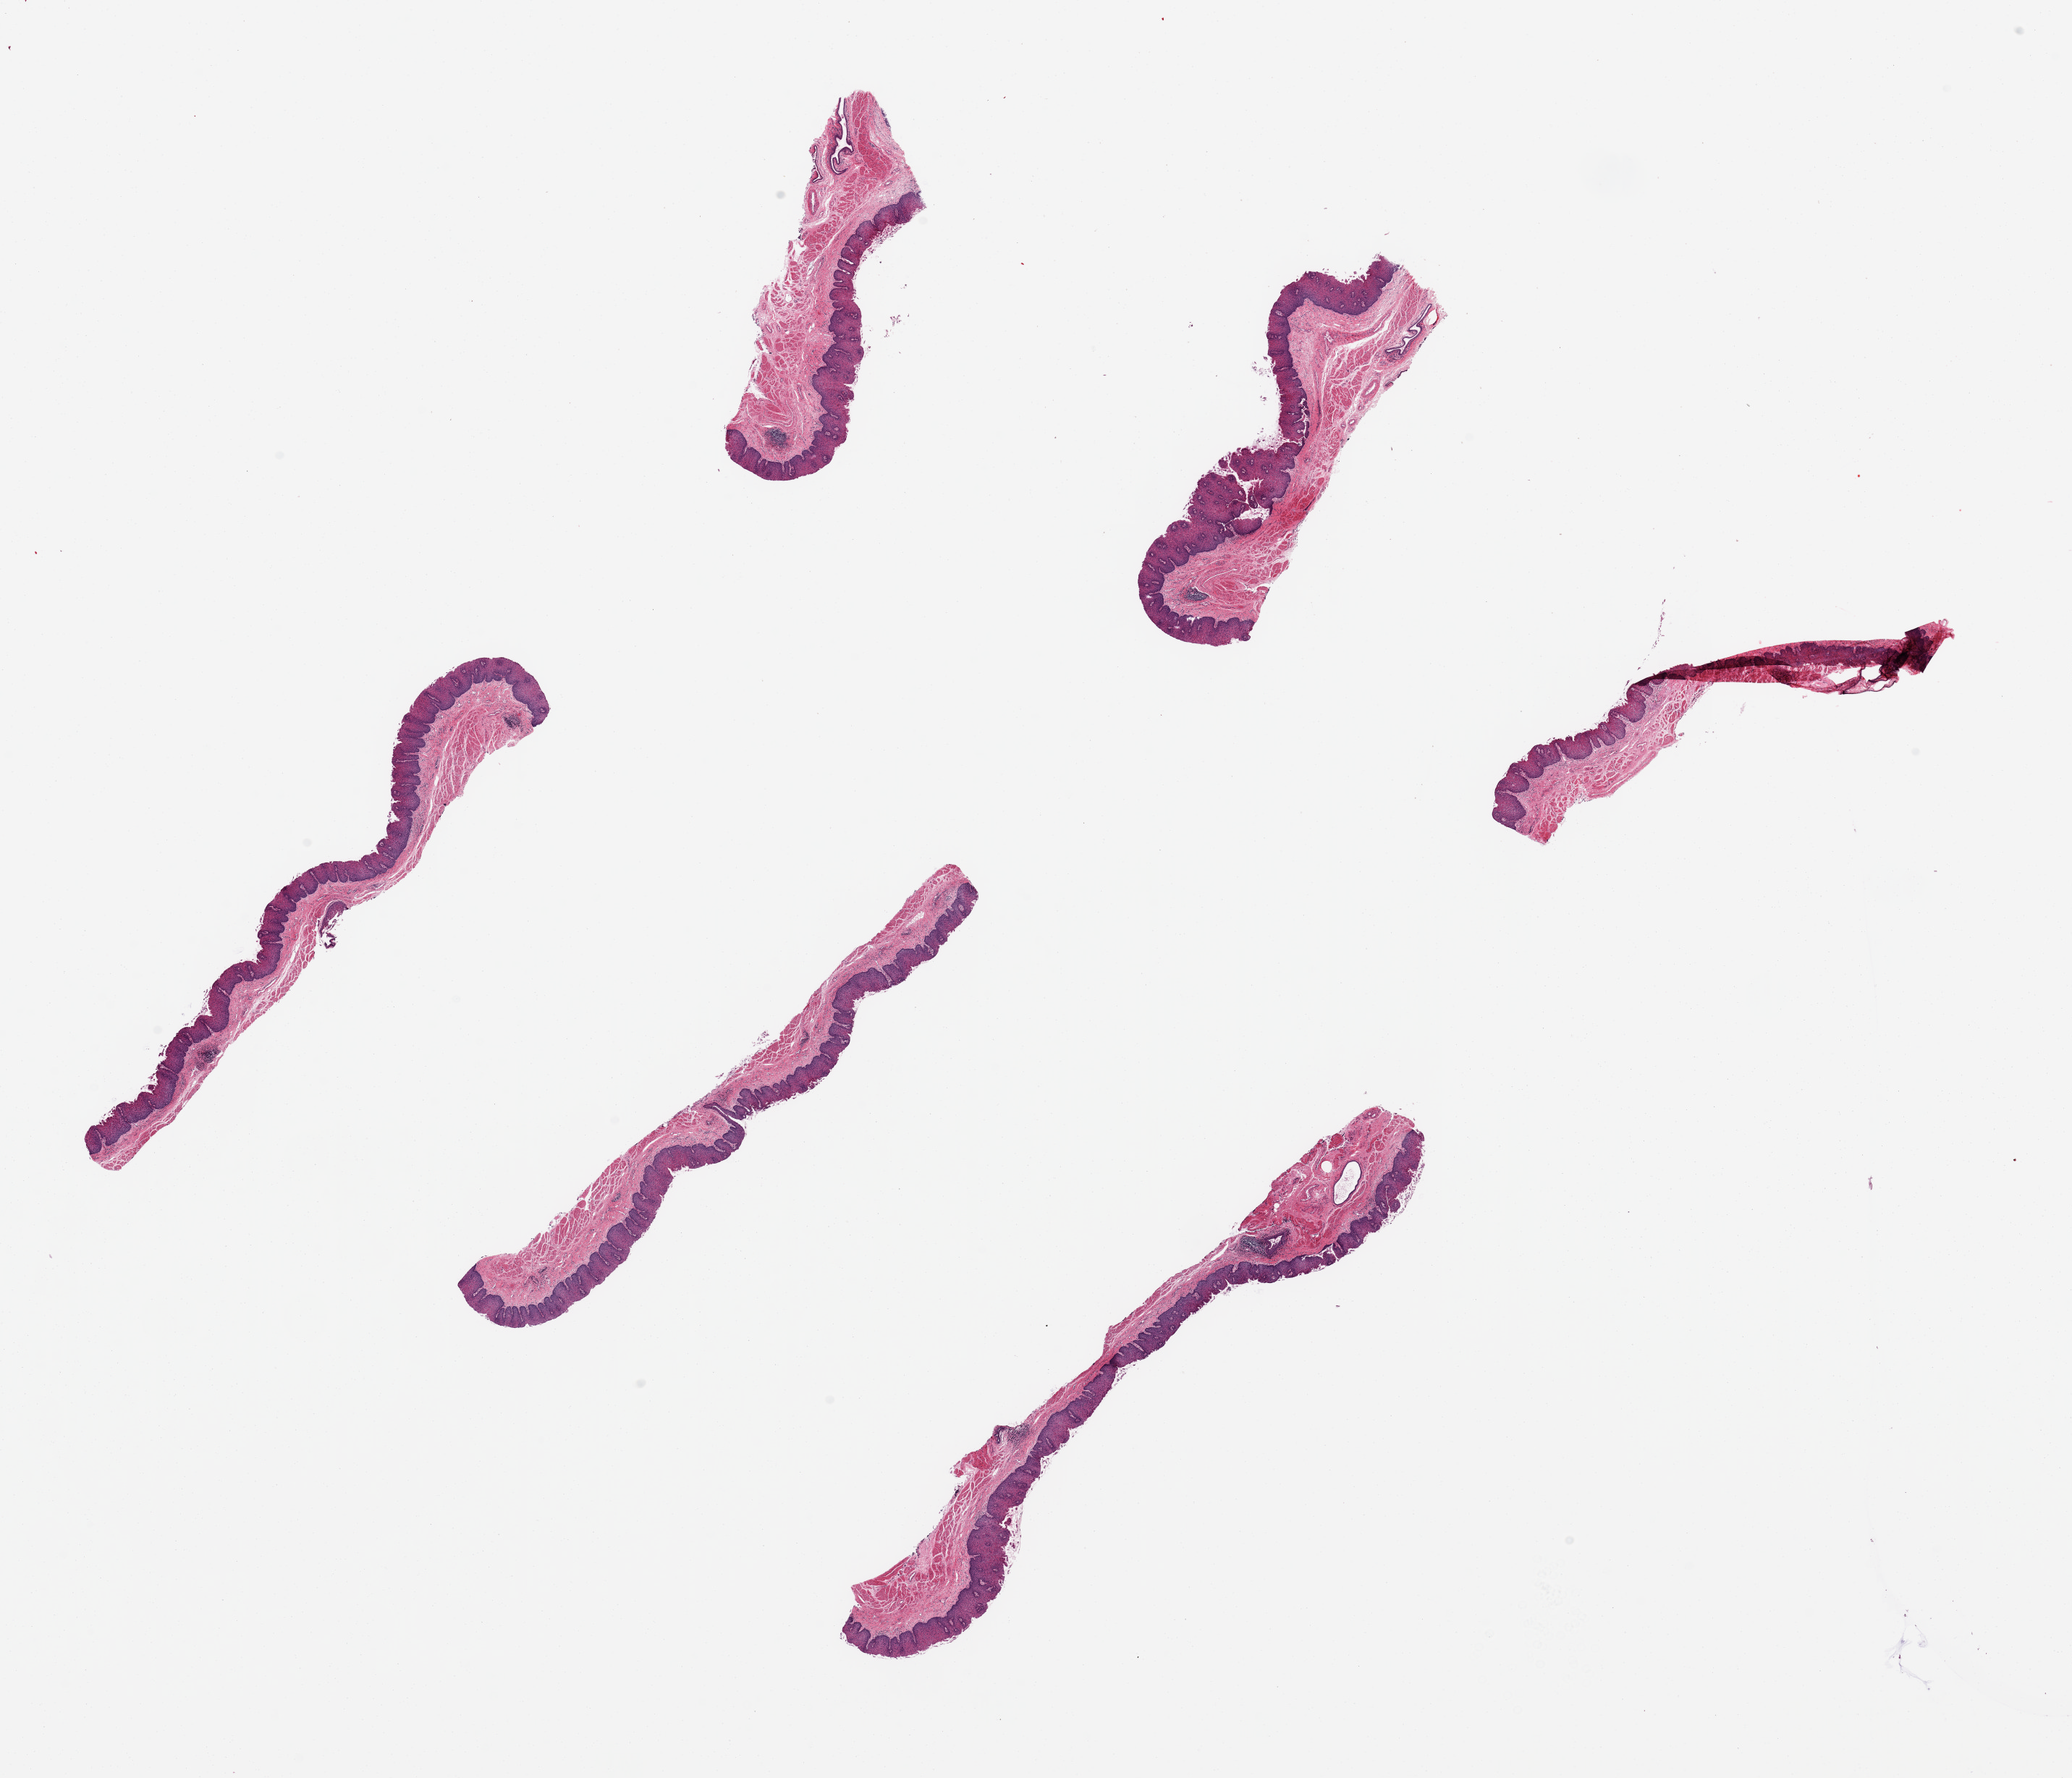
Digitized haematoxylin and eosin-stained section, brightfield, a low-resolution overview of the entire scanned area, about 22.6 x 19.4 mm (acquisition: 20x scan); PAXgene-fixed, paraffin-embedded tissue; sampled site (target tissue): esophageal mucous membrane; tissue donor sample. Donor sex: male.
Review note (as recorded): 6 pieces, ~8x1.3 mm; mucosa=~0.25mm thick. Well preserved mucosa.